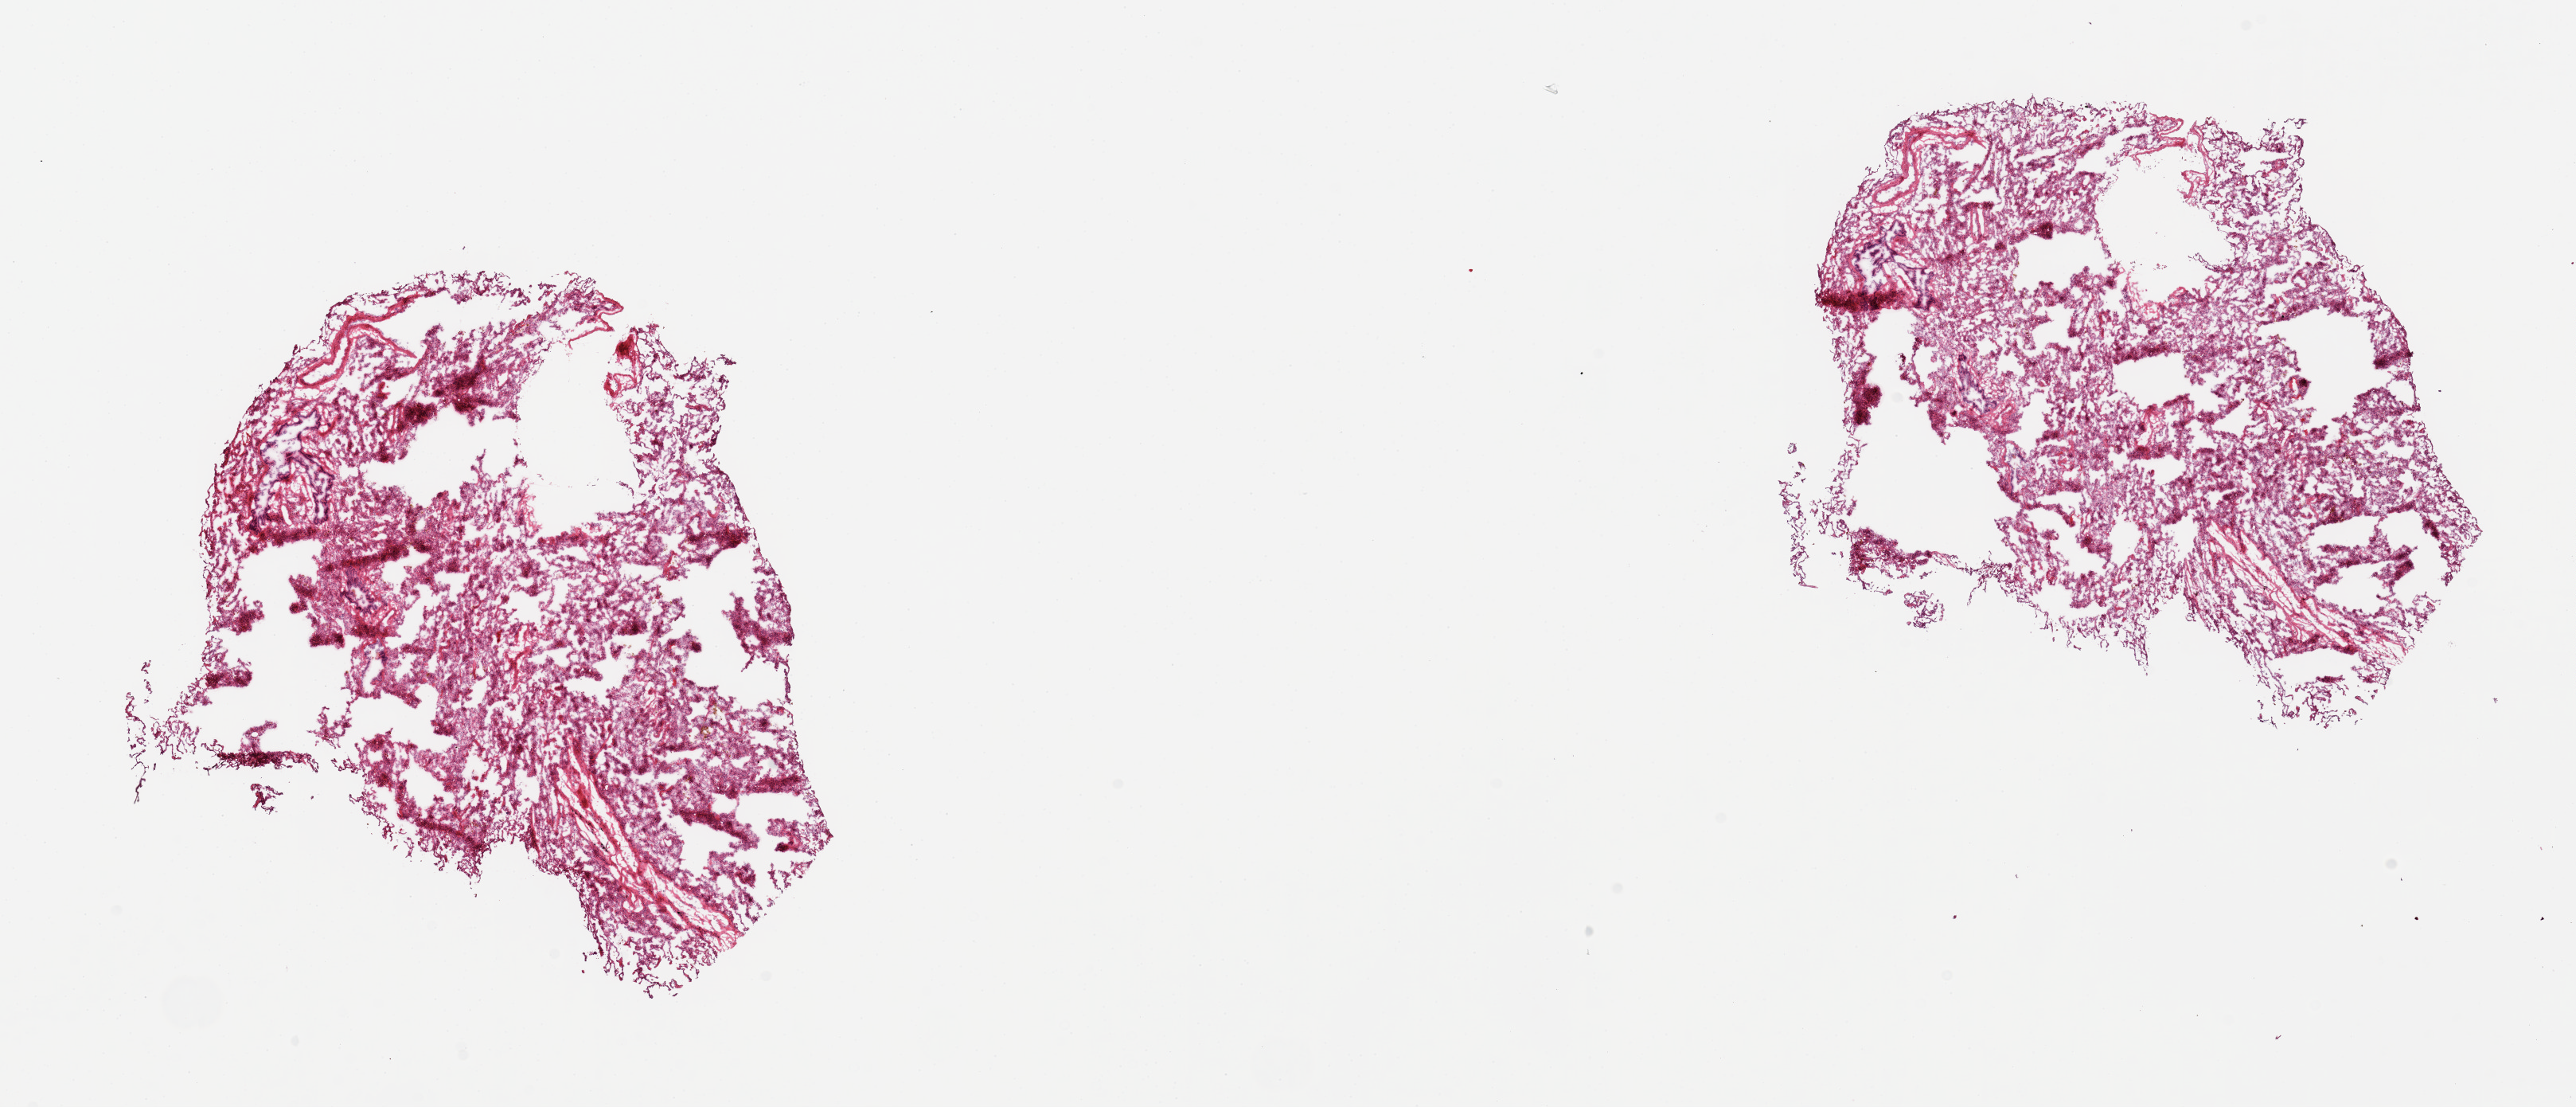
H&E whole-slide image, a low-resolution overview of the entire scanned area, about 25.6 x 11.0 mm (acquisition: 20x scan). Donor sex: female.
Specimen: frozen section (dry ice); sampled site (target tissue): lung; donor tissue sample.